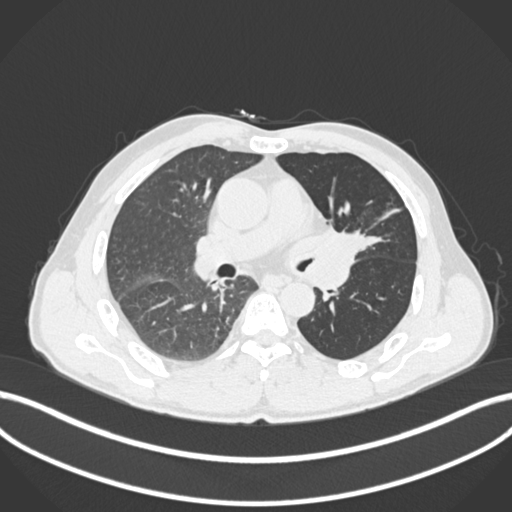
Chest CT, one axial slice; slice 105 of 255 in the series (ordered by position); 120 kVp; lung window (W 1500 / L -600 HU); 1 mm slice thickness; 512 × 512 image matrix, field of view 400 × 400 mm. Patient: male, 57 years. From the clinical record (not read from this slice): clinical TNM (as recorded): T2b N0 M0.
Structures marked on this image (rectangle marked by the reading radiologist):
- lung tumour (recorded histology: squamous cell carcinoma): bounding box (x1, y1, x2, y2) in pixels: (319, 223, 375, 259)